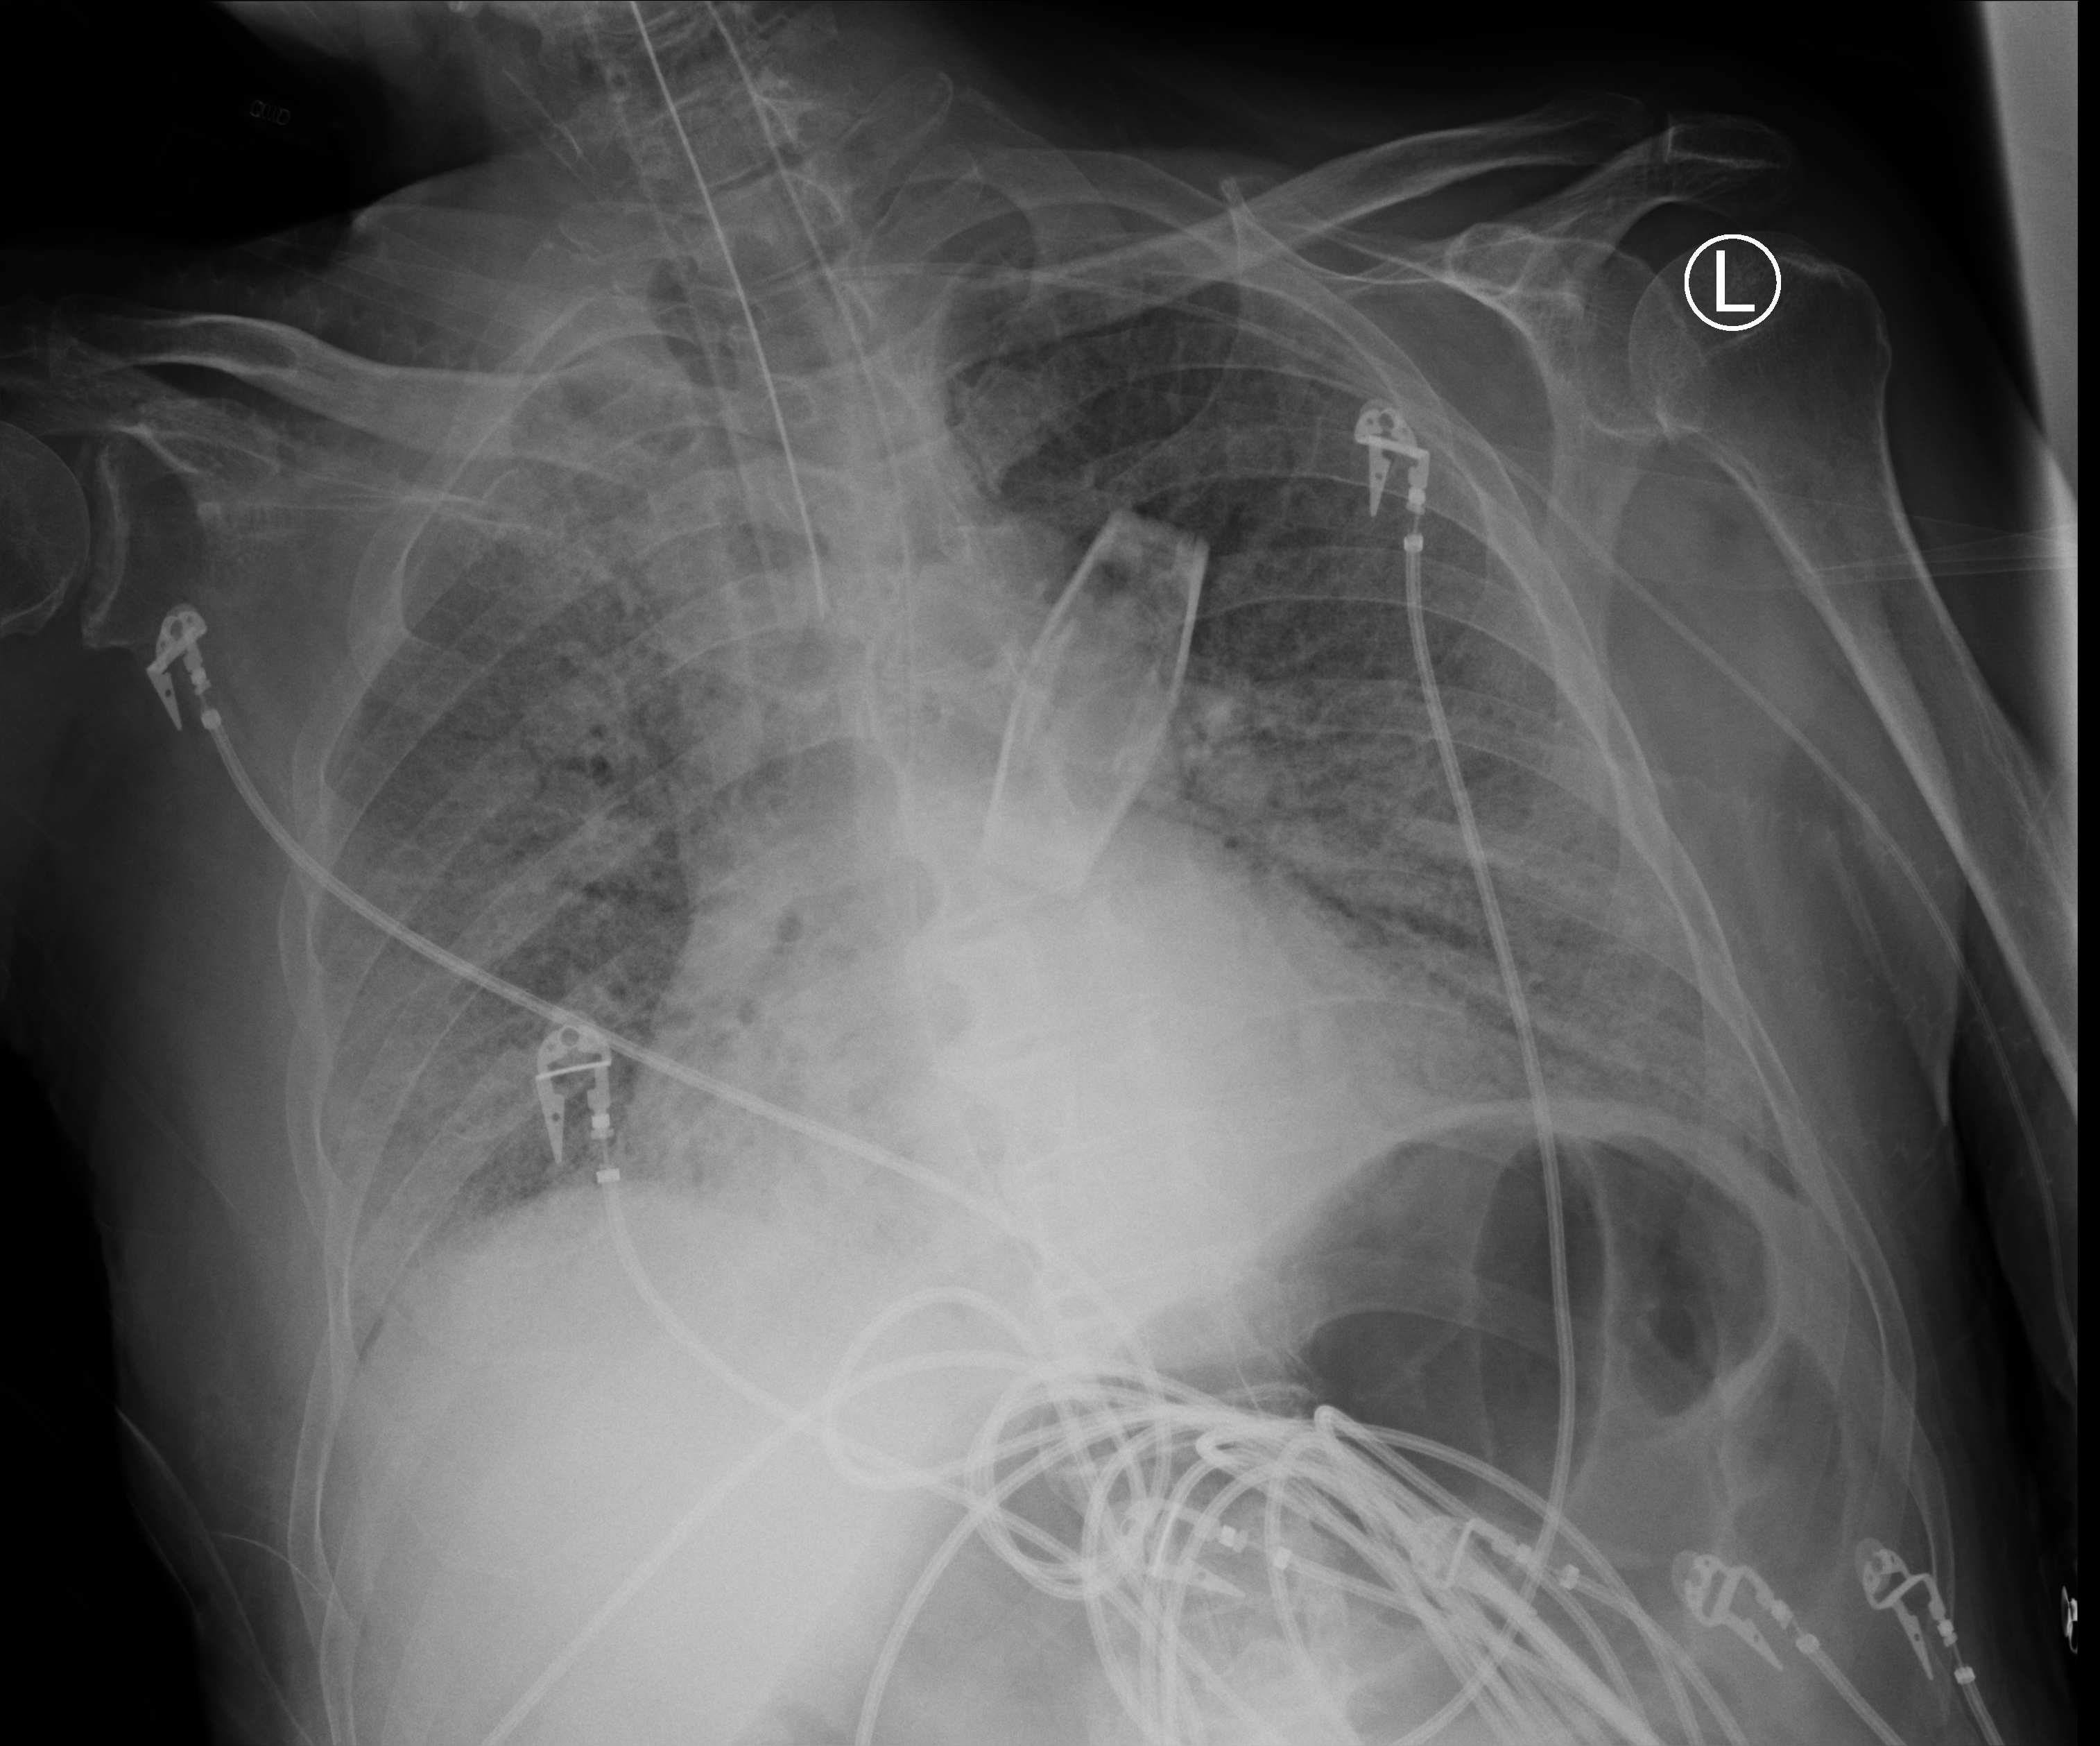
Chest X-ray (portable); anteroposterior (AP) projection. Patient hospitalised with COVID-19; male, aged 75–90 years.
Admission-level facts for this patient (not findings on this image; timing relative to this image not recorded): admitted to intensive care during this hospital stay: yes; mechanically ventilated during this hospital stay: yes; chronic kidney disease (admission record): no.